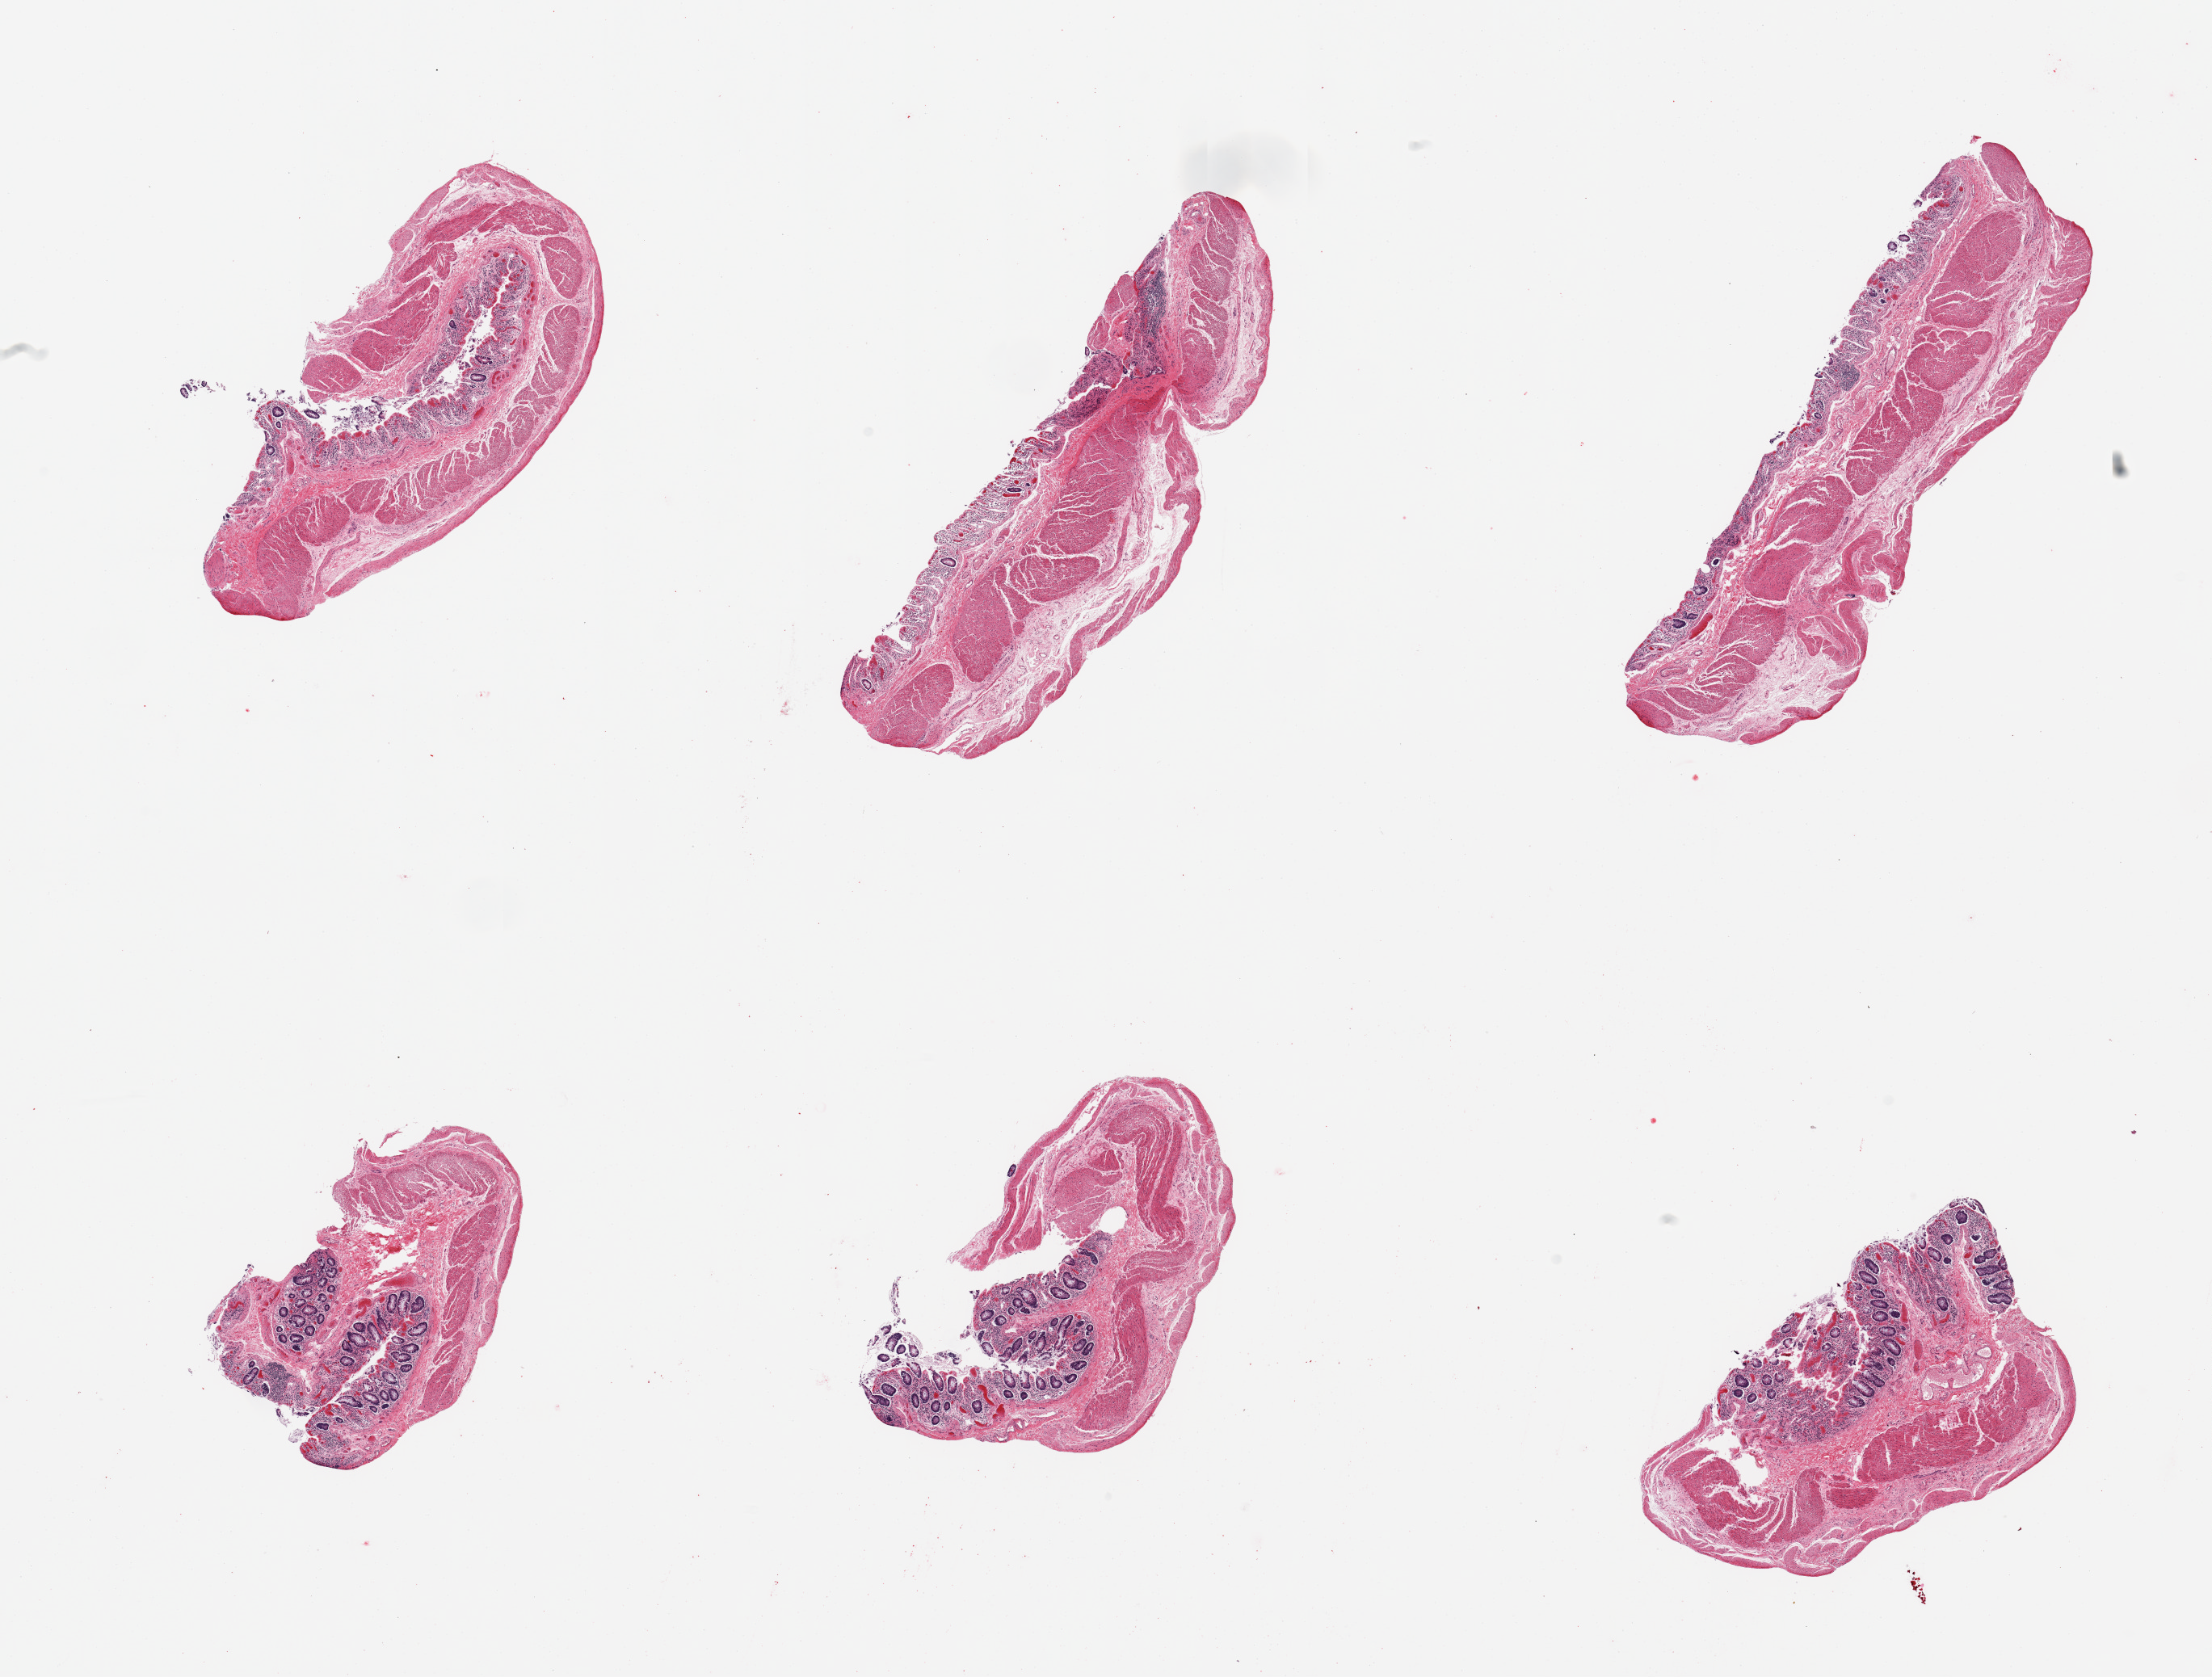
Whole-slide image, hematoxylin and eosin (H&E) stain — shown as a low-resolution overview of the whole scanned area (about 21.7 x 16.4 mm, slide scanned at 20x); PAXgene-fixed paraffin-embedded (PFPE) section; section of transverse colon (target tissue); tissue donor sample.
Reviewer comment on this tissue sample: 6 pieces, mucosa largely sloughed, advanced autolysis.